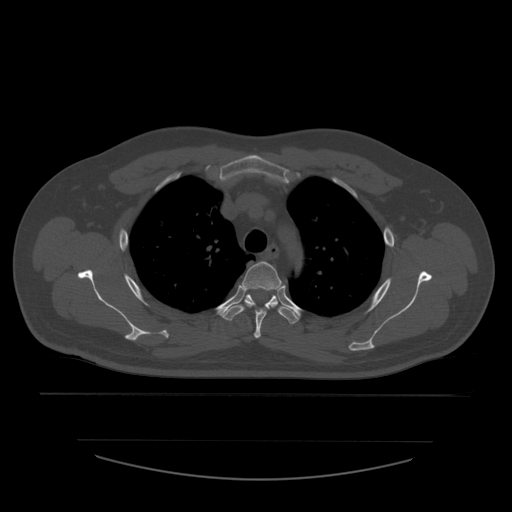
CT including the spine, one axial slice; slice 426 of 532 in the series (ordered by position); 120 kVp; bone window (W 1800 / L 400 HU); 512 × 512 image matrix, field of view 441 × 441 mm. Patient age 44 years. Case-level facts recorded for this patient, not image findings: primary cancer: soft tissue sarcoma.
Structures marked on this image (semi-automatic segmentation, software-assisted and operator-edited):
- T3 vertebra: bounding box <242,262,282,339> (left, top, right, bottom; pixels)
- T4 vertebra: <221,294,299,325>